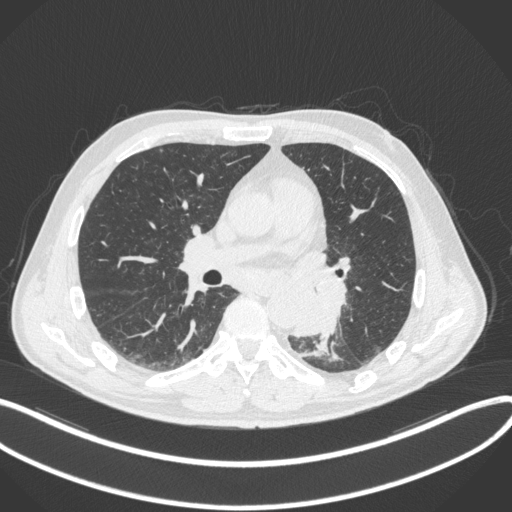
Chest CT, one axial slice. Reconstruction kernel B31f. 120 kVp. Lung window (W 1500 / L -600 HU). 1 mm slice thickness. 512 × 512 image matrix, field of view 400 × 400 mm. Male patient, age 59 years. Case-level facts recorded for this patient, not image findings: clinical TNM (as recorded): T2a N2 M0.
Structures marked on this image (rectangle marked by the reading radiologist):
- lung tumour (recorded histology: squamous cell carcinoma): bounding box [x1, y1, x2, y2] px = [288, 278, 346, 337]